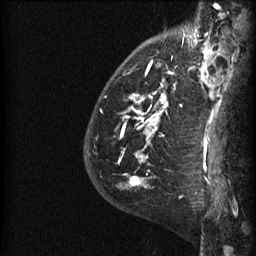
Breast MRI (dynamic contrast-enhanced), one sagittal slice; position 12 of 60 along the scan axis; dynamic contrast-enhanced series, image 2 of 3 at this slice position (ordered by acquisition); 1.5 T; TE 4.2 ms, TR 22.7 ms; 1.5 mm slice thickness; 256 × 256 image matrix, field of view 180 × 180 mm. Female patient, age 48 years. From the clinical record (not read from this slice): setting: breast cancer imaged before/during neoadjuvant chemotherapy; receptor status: triple-negative.
Annotated regions visible in this slice (semi-automatically segmented with operator editing):
- analysis volume of interest (the breast-tissue region the enhancement analysis was run in; not a lesion): box from (x=89, y=27) to (x=191, y=180) px
- tumour enhancement mask (voxels above the 90 % enhancement threshold inside the analysis volume of interest): (x=122, y=60)–(x=175, y=180)